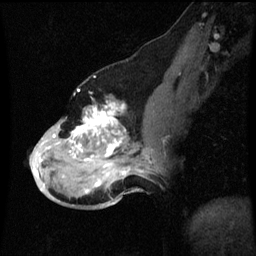
Breast MRI (dynamic contrast-enhanced), one sagittal slice; position 30 of 60 along the scan axis; dynamic contrast-enhanced series, image 2 of 3 at this slice position (ordered by acquisition); 1.5 T; TE 4.2 ms, TR 8.9 ms; 2 mm slice thickness; 256 × 256 image matrix, field of view 200 × 200 mm. Patient: female, 49 years. From the clinical record (not read from this slice): setting: breast cancer imaged before/during neoadjuvant chemotherapy; receptor status: HR-positive, HER2-negative.
Structures marked on this image (semi-automatically segmented with operator editing):
- analysis volume of interest (the breast-tissue region the enhancement analysis was run in; not a lesion): bounding box (x1, y1, x2, y2) in pixels: (32, 100, 159, 199)
- tumour enhancement mask (voxels above the 70 % enhancement threshold inside the analysis volume of interest): (34, 104, 143, 187)